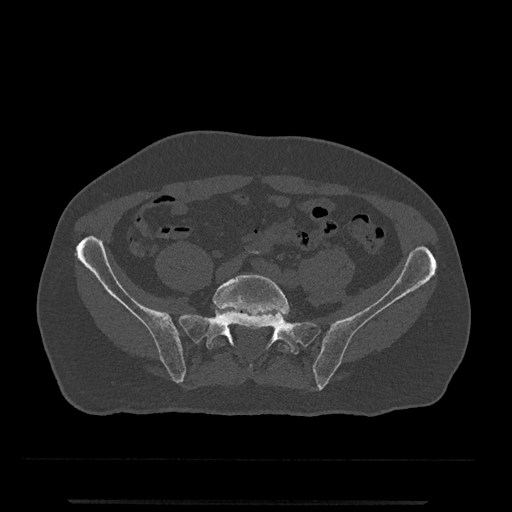
CT including the spine, one axial slice; position 39 of 797 along the scan axis; reconstruction kernel Br40s/3; bone window (W 1800 / L 400 HU); 0.5 mm slice thickness; 512 × 512 image matrix, field of view 419 × 419 mm. Male patient, age 63 years. From the clinical record (not read from this slice): primary cancer: prostate.
Structures marked on this image (semi-automatically segmented with operator editing):
- L5 vertebra: bounding box (x1, y1, x2, y2) in pixels: (209, 274, 289, 352)